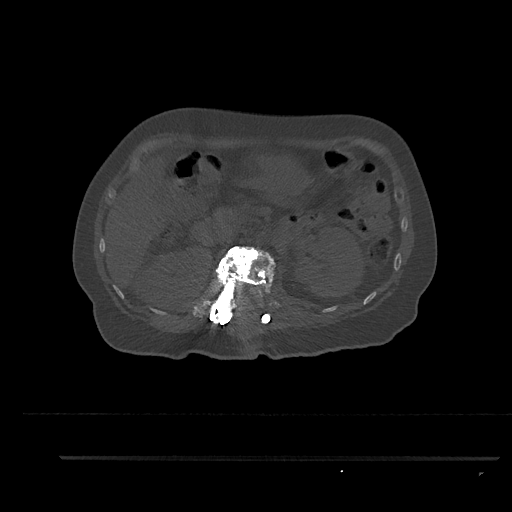
CT including the spine, one axial slice; slice 217 of 797 in the series (ordered by position); reconstruction kernel Br40s/3; 120 kVp; bone window (W 1800 / L 400 HU); 0.5 mm slice thickness; 512 × 512 image matrix, field of view 408 × 408 mm. Patient: female, 44 years. From the clinical record (not read from this slice): primary cancer: renal; vertebrae with lytic lesions (as recorded): L1.
Outlined on this slice (semi-automatically segmented with operator editing):
- L1 vertebra: bounding box <208,246,276,320> (left, top, right, bottom; pixels)